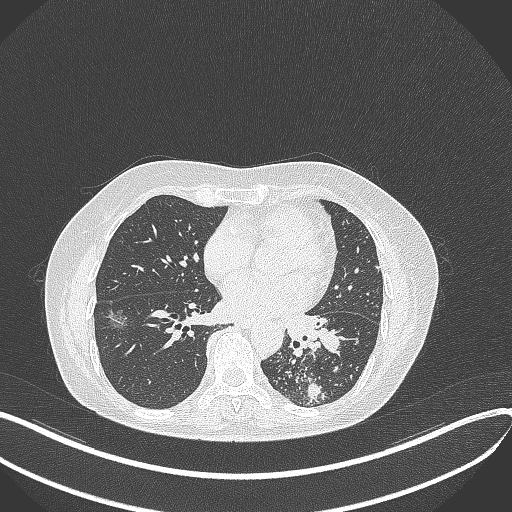
Chest CT, one axial slice; slice 175 of 429 in the series (ordered by position); reconstruction kernel B70f; lung window (W 1500 / L -600 HU); 512 × 512 image matrix, field of view 400 × 400 mm. Patient: female, 63 years. From the clinical record (not read from this slice): clinical TNM (as recorded): T1b N0 M0.
Outlined on this slice (bounding box drawn by a radiologist):
- lung tumour (recorded histology: adenocarcinoma): bounding box (x1, y1, x2, y2) in pixels: (281, 307, 345, 356)